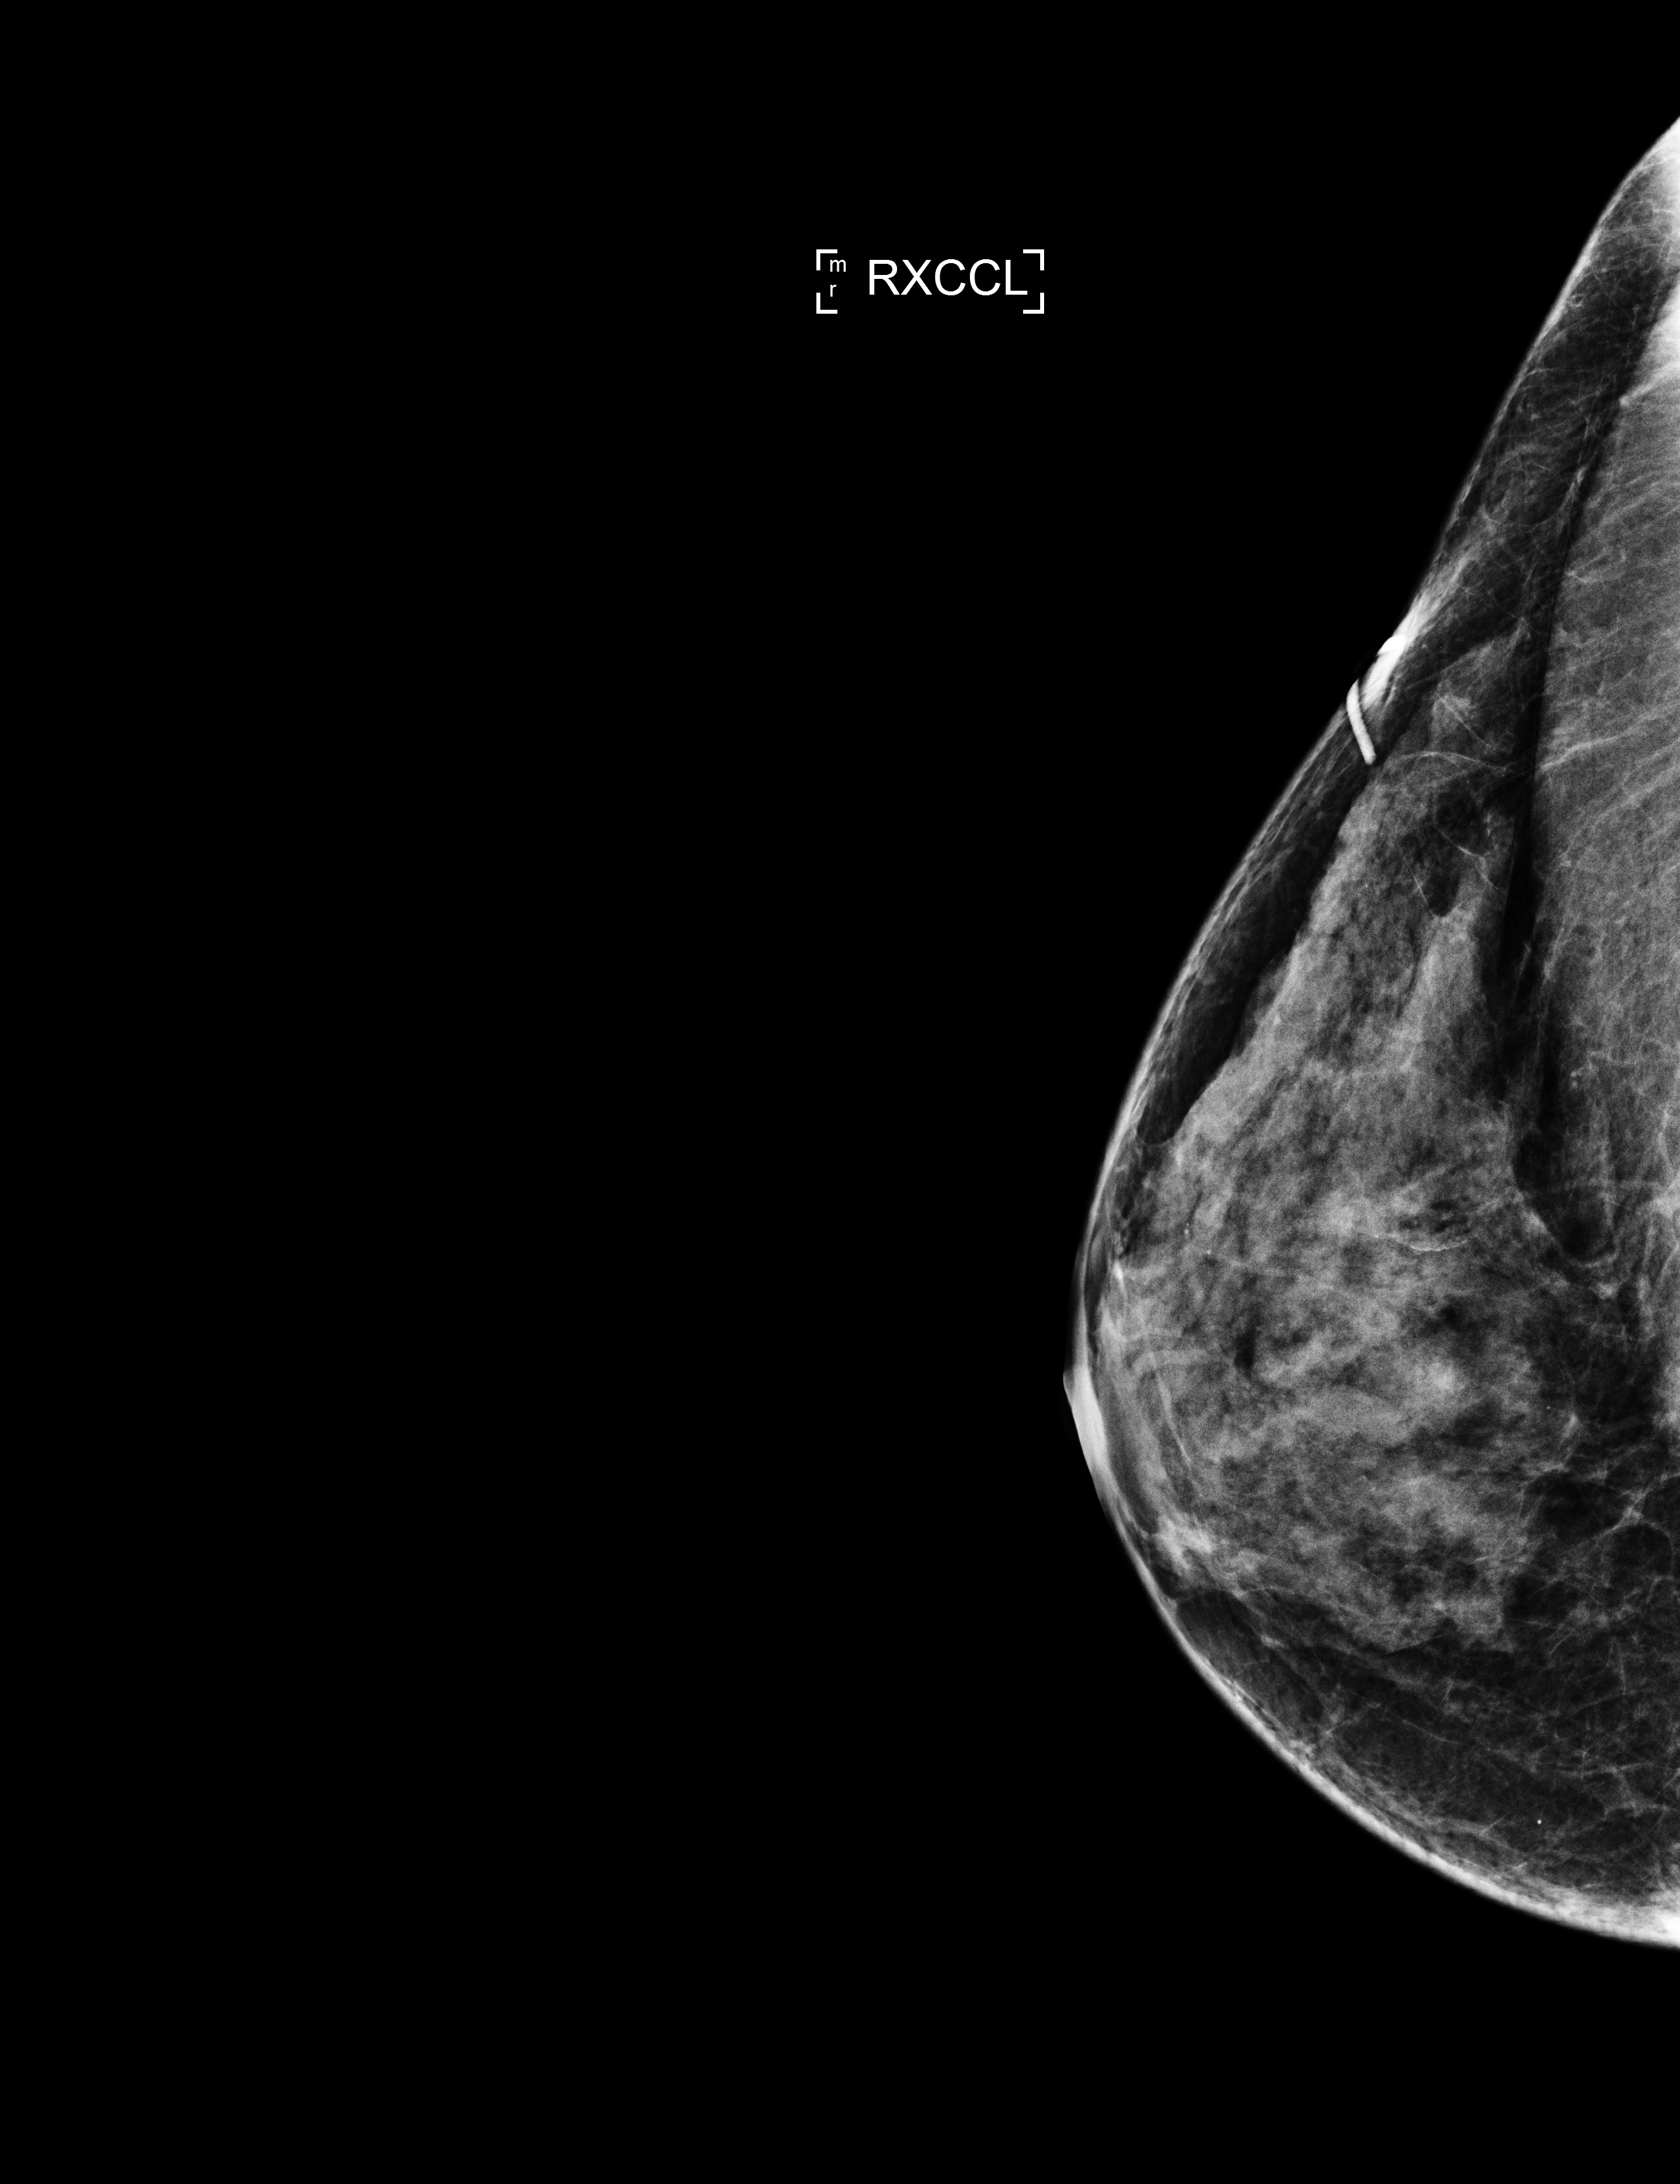
Annual screening mammography examination. Patient: female, 51 years.
Image type: full-field digital mammogram. Breast: right. Projection: exaggerated CC view (lateral).